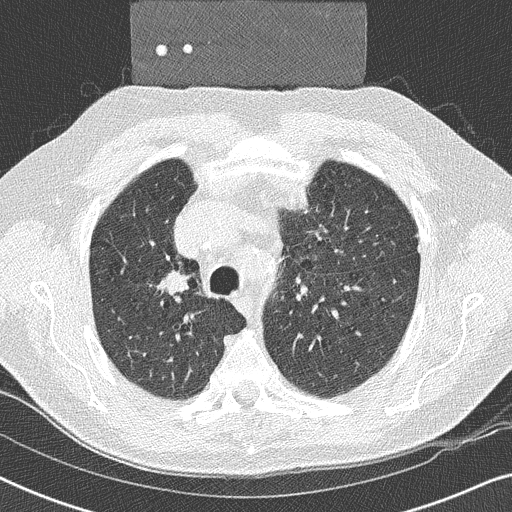
Chest CT (low-dose screening protocol), one axial image; second screening round (one year after baseline); lung window (W 1500 / L -600 HU); 512 × 512 image matrix, field of view 330 × 330 mm. Male participant, aged 59 years at enrolment.
- Lesion marked by an expert reader, bounding box [x1, y1, x2, y2] px = [148, 258, 206, 308].
- The exam's reader record, not a measurement of the box and not confirmed to be the same lesion: non-calcified nodule or mass ≥4 mm, right upper lobe, 17 × 16 mm, smooth margins, soft tissue attenuation, pre-existing on the prior screen: yes.
- Official screen result: positive, other.